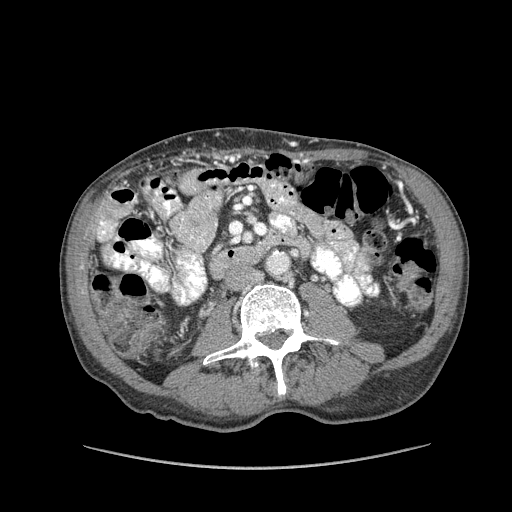
Contrast-enhanced abdominal CT (liver protocol), one axial slice; position 1 of 162 along the scan axis; reconstruction kernel STANDARD; soft-tissue window (W 400 / L 40 HU); 2.5 mm slice thickness; 512 × 512 image matrix, field of view 400 × 400 mm. Case-level facts recorded for this patient, not image findings: diagnosis: hepatocellular carcinoma (patient treated with transarterial chemoembolisation; whether this scan precedes or follows treatment is not stated here); TNM stage (as recorded): Stage-IIIA; Child-Pugh class: A; tumour nodularity: multinodular.
Structures marked on this image (semi-automatically segmented with operator editing):
- liver parenchyma outside the tumour (the mass and vessels are separate outlines, so this box may not span the whole liver): bounding box (x1, y1, x2, y2) in pixels: (96, 216, 114, 242)
- liver vessels: (98, 221, 113, 239)